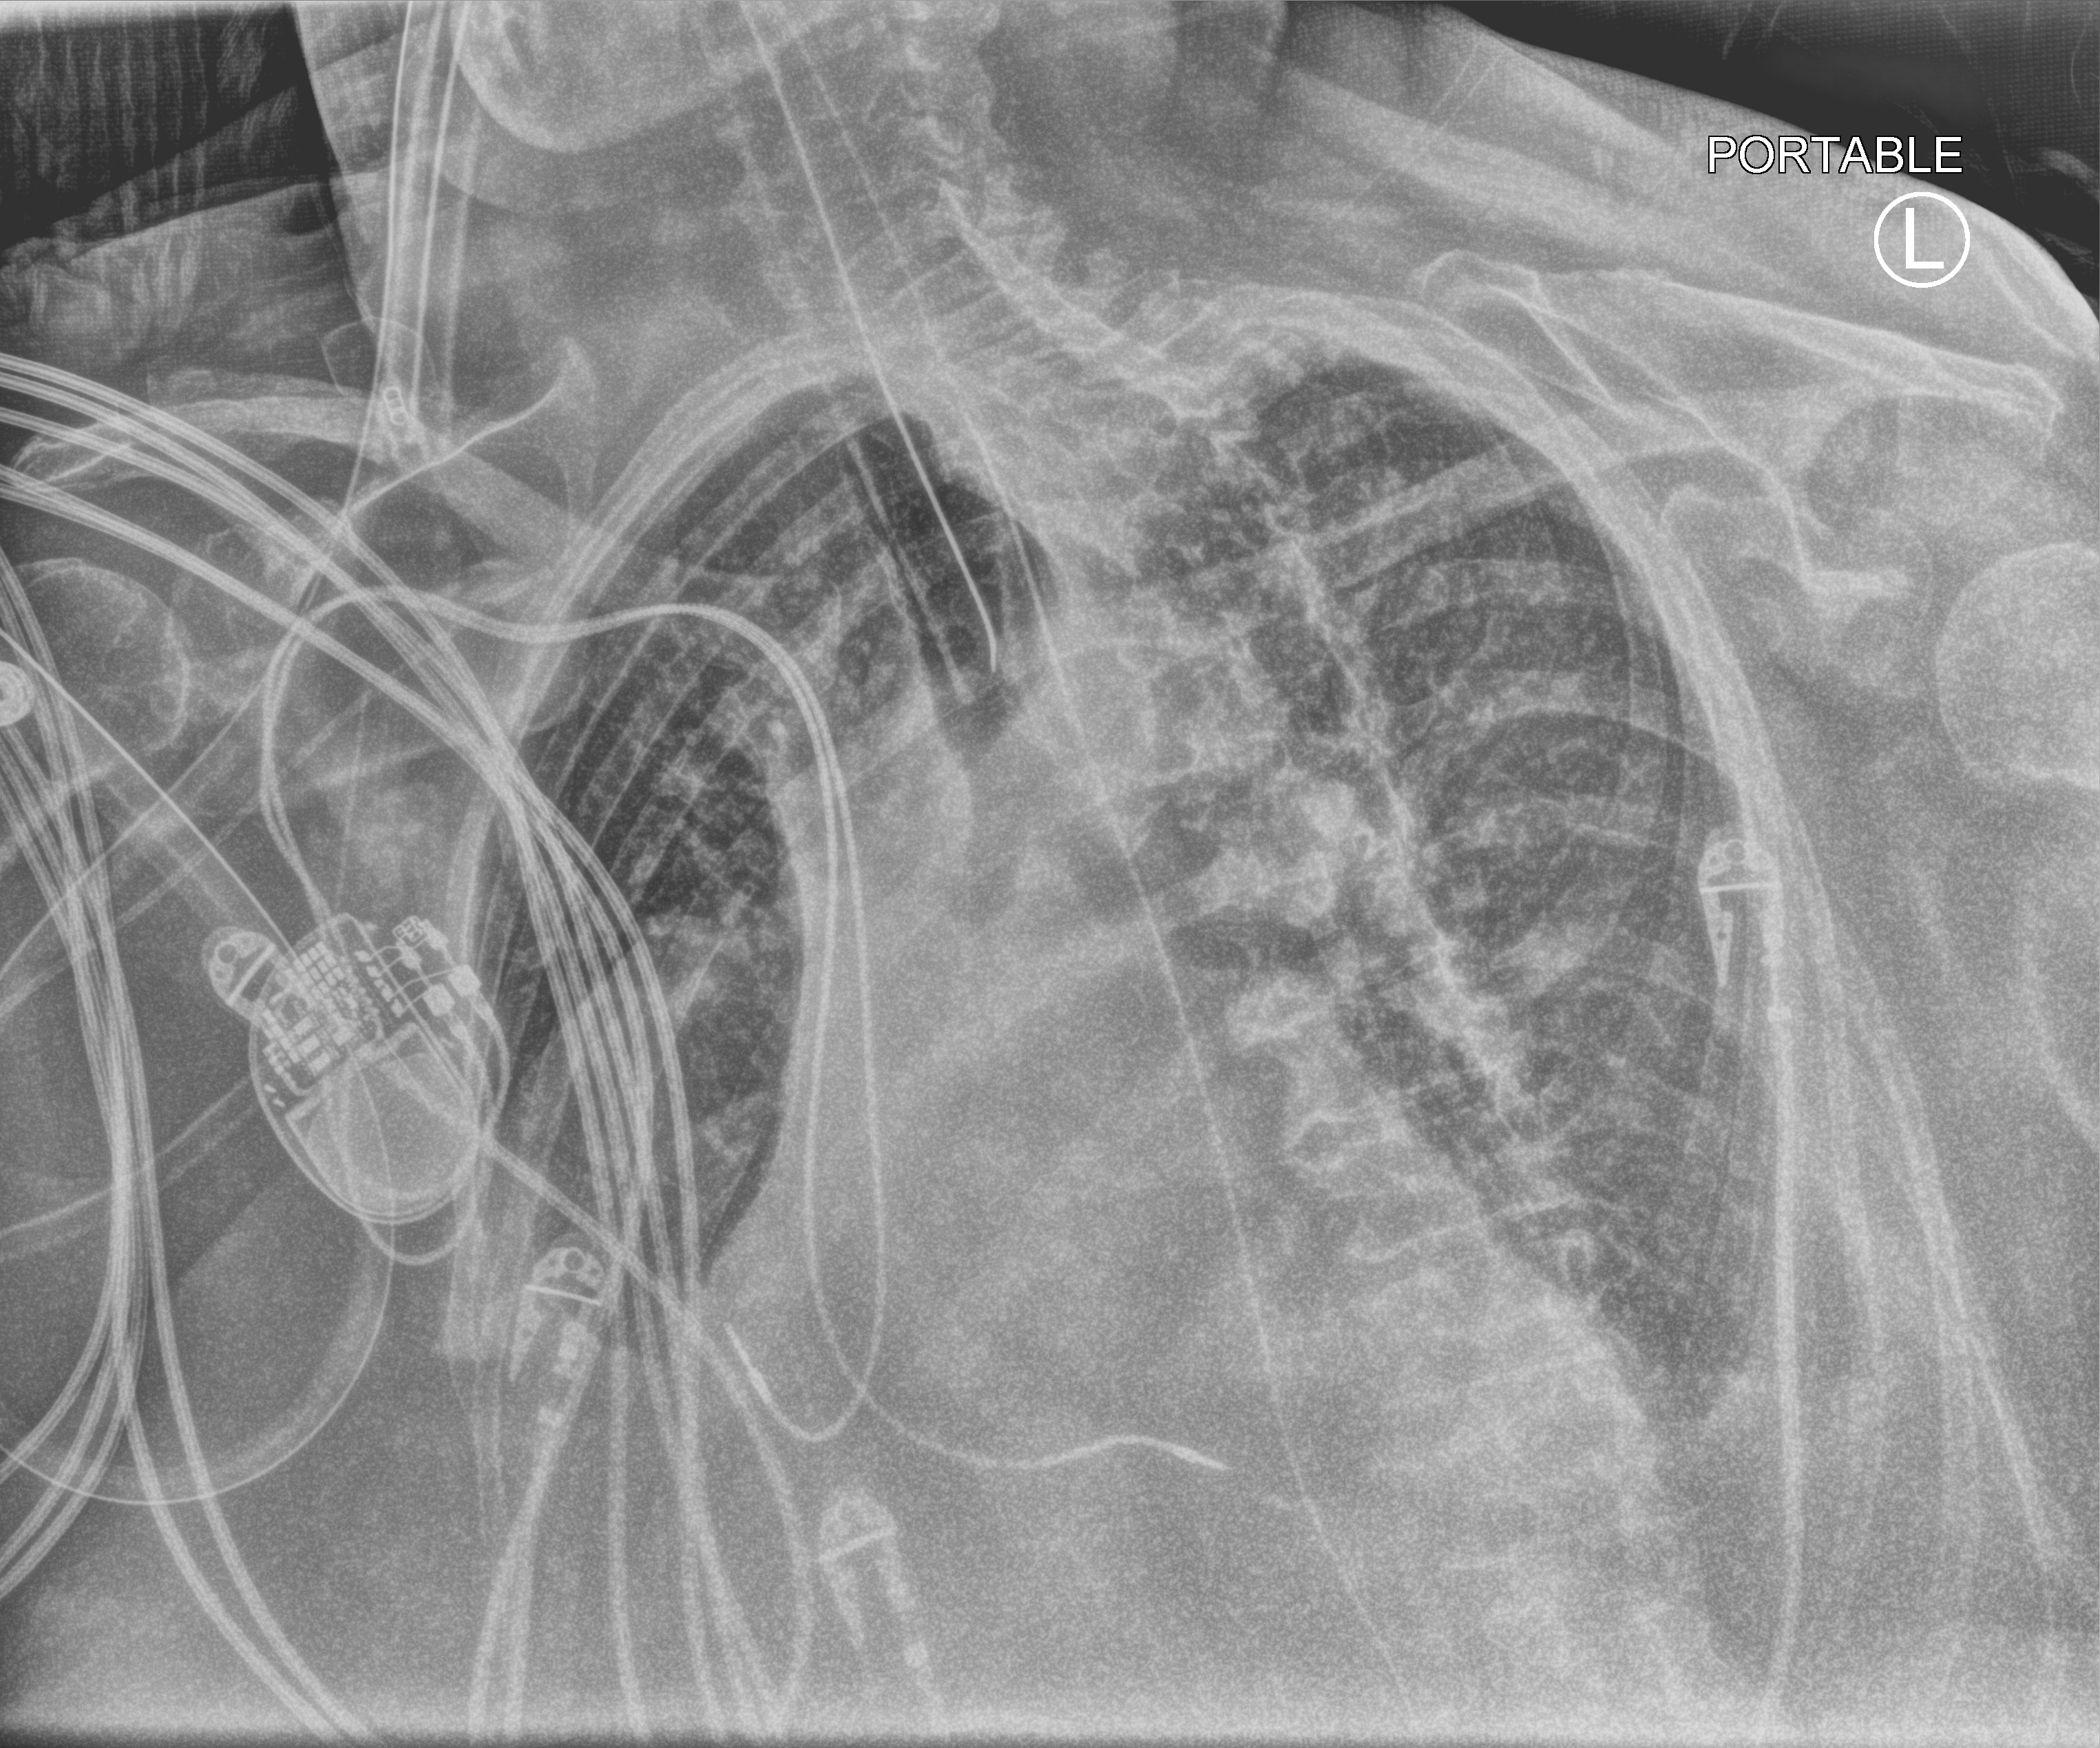
Portable chest radiograph. Female patient hospitalised with COVID-19, age 75–90 years.
Admission-level facts for this patient (not findings on this image; timing relative to this image not recorded): mechanically ventilated during this hospital stay: yes; admitted to intensive care during this hospital stay: yes.